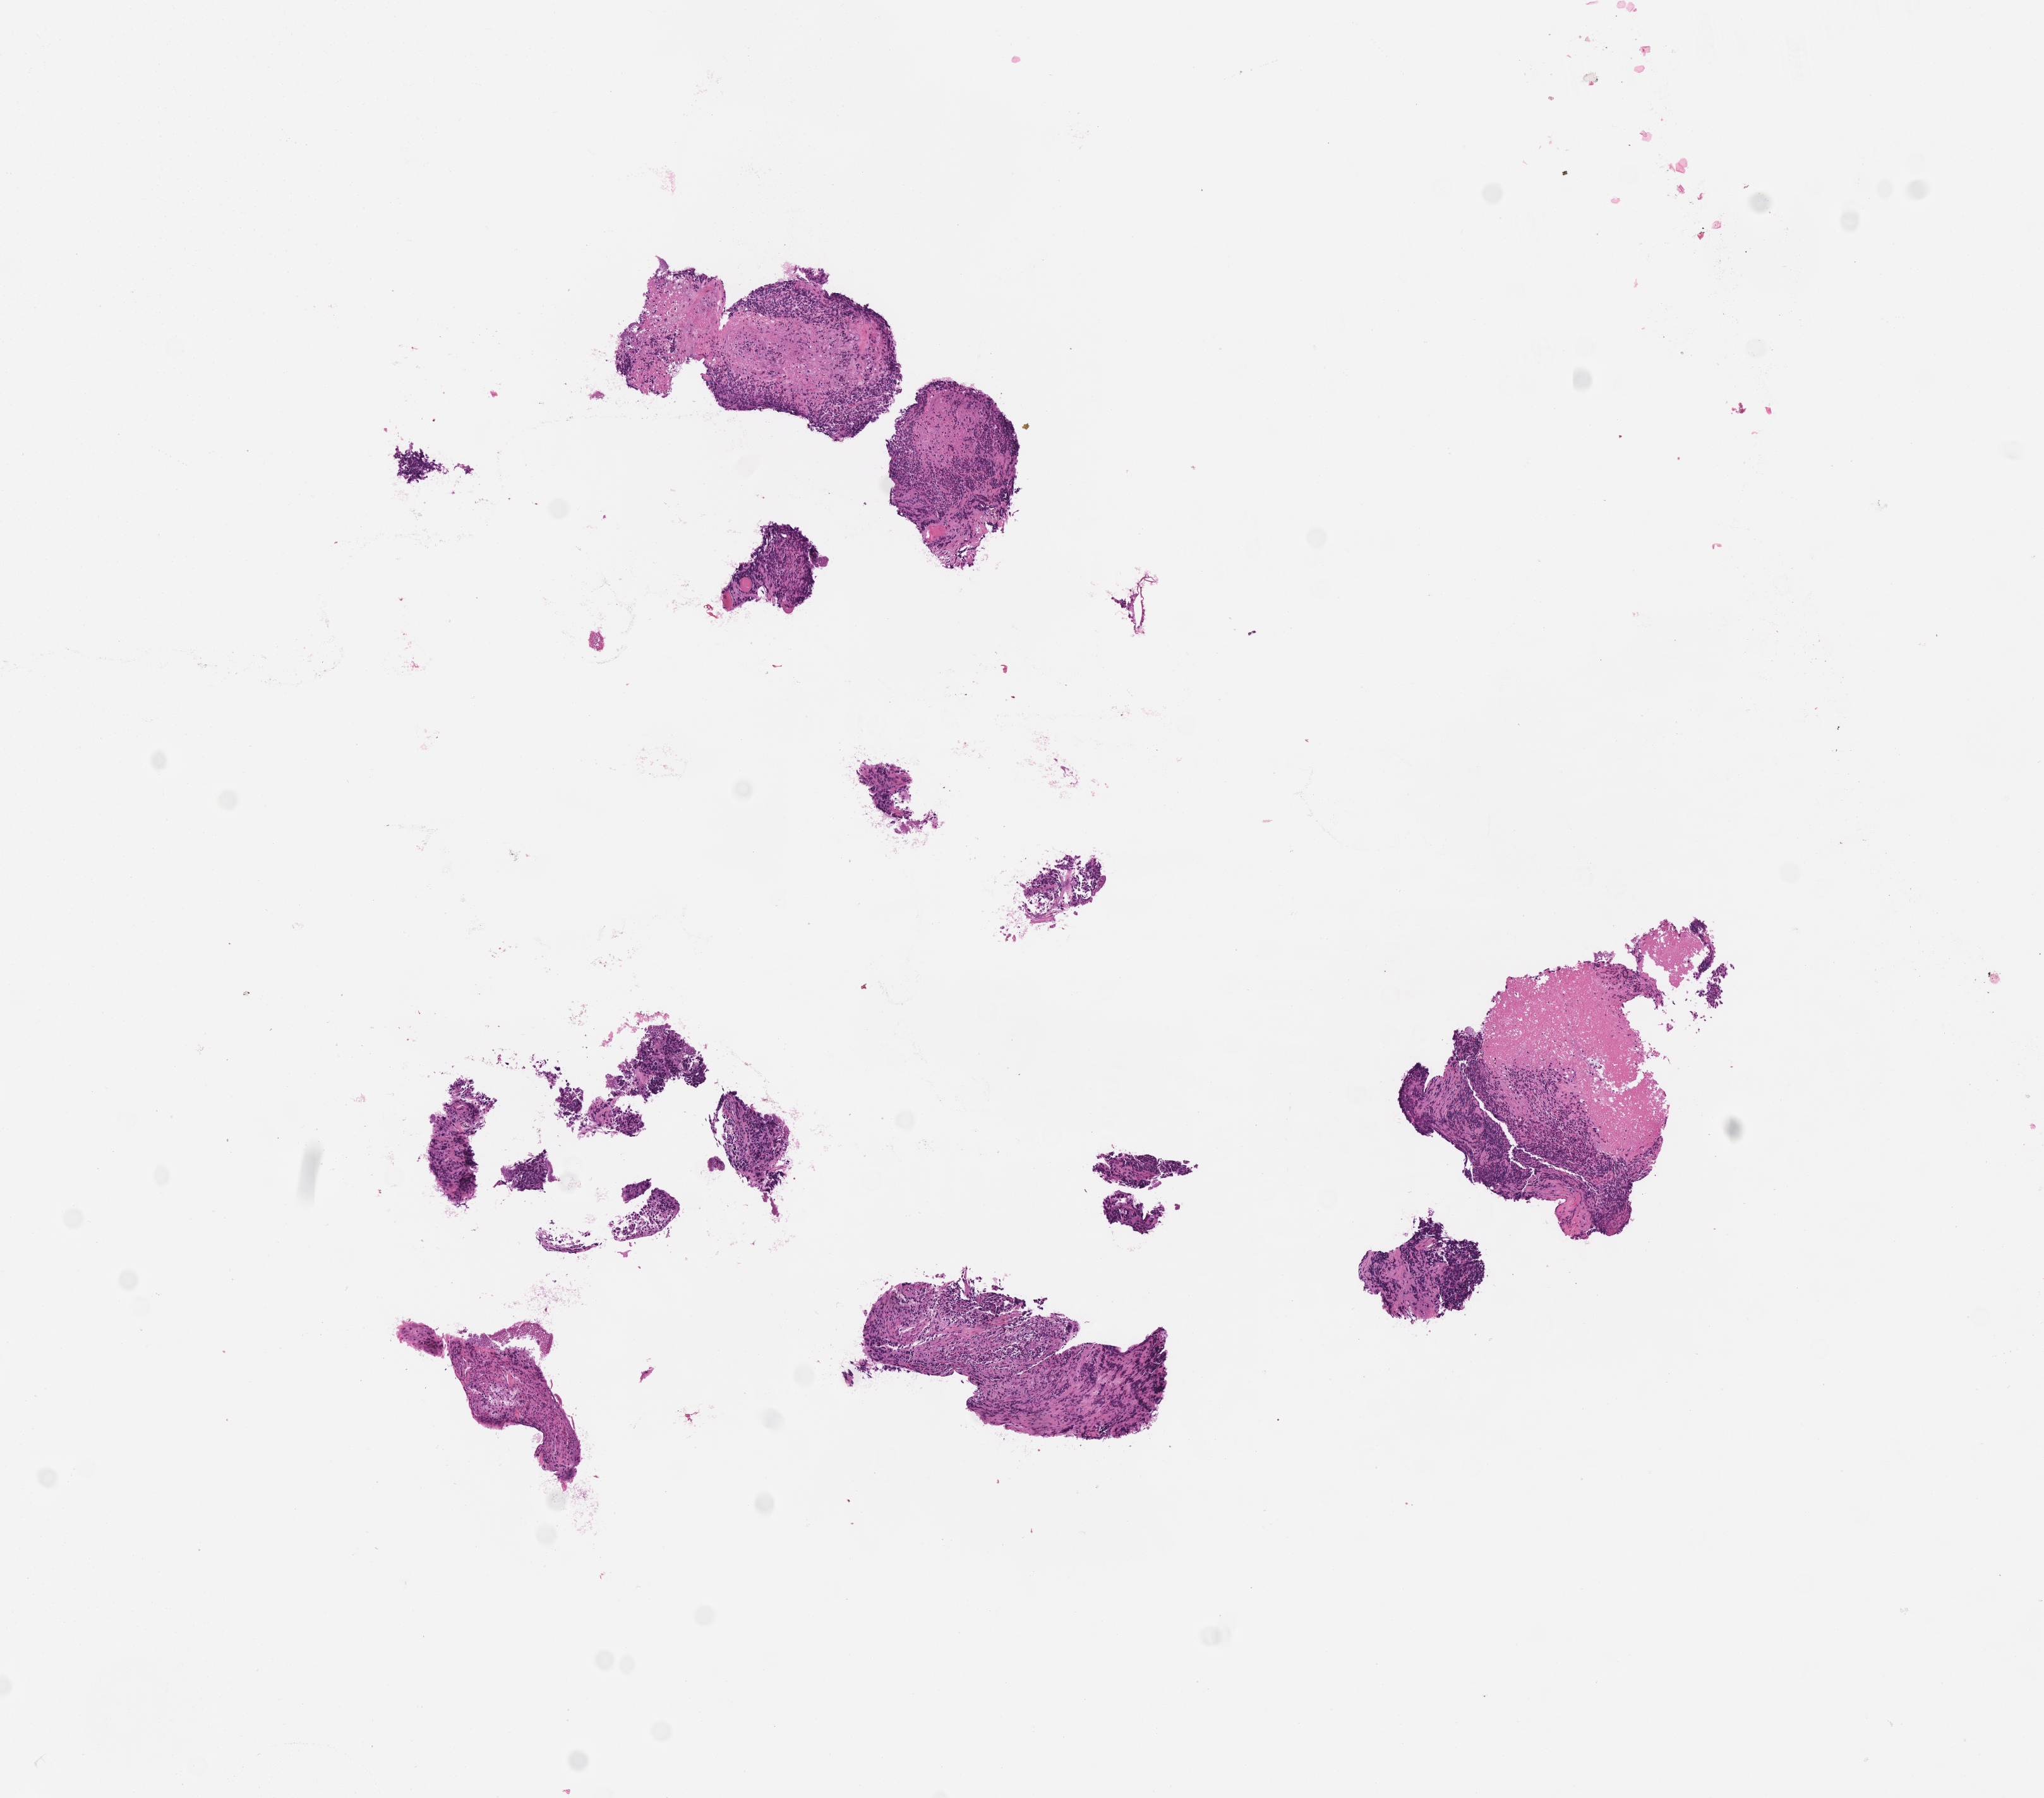
Haematoxylin and eosin whole-slide image of tumor tissue — whole scanned area (about 6.5 x 5.8 mm) shown as a low-resolution overview. Formalin-fixed, paraffin-embedded (FFPE) tissue. Site: soft tissue, forearm-right. Patient: female, age 15.2 years at diagnosis.
- stage (as recorded): 4
- diagnosis: rhabdomyosarcoma; histological classification: alveolar rhabdomyosarcoma